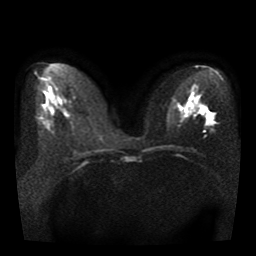
Breast MRI, one axial slice; slice 19 of 41 in the series (ordered by position); diffusion-weighted series; image 2 of 4 stored at this slice position (different b-values; order by instance number); 1.5 T; 5 mm slice thickness; 256 × 256 image matrix. Female patient.
Structures marked on this image (outlined manually by an expert reader):
- tumour on diffusion-weighted imaging: bounding box <207,111,210,116> (left, top, right, bottom; pixels)